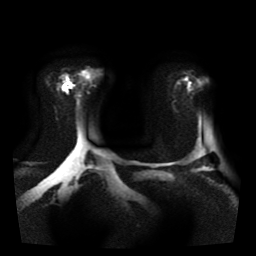
Breast MRI, one axial slice. Slice 28 of 41 in the series (ordered by position). Diffusion-weighted series; image 2 of 4 stored at this slice position (different b-values; order by instance number). 1.5 T. 256 × 256 image matrix, field of view 330 × 330 mm. Female patient.
Structures marked on this image (manually delineated by an expert):
- tumour on diffusion-weighted imaging: bounding box (x1, y1, x2, y2) in pixels: (63, 76, 74, 93)